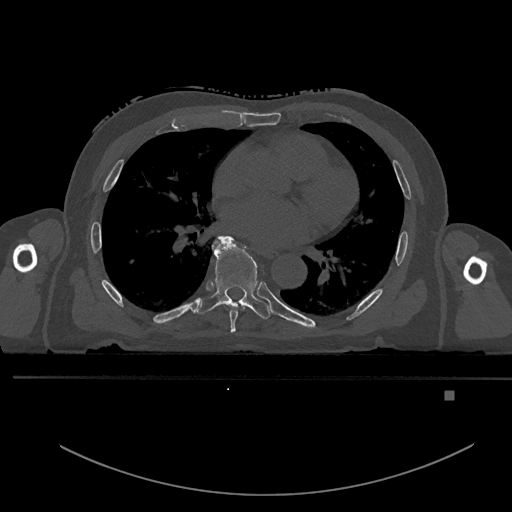
CT including the spine, one axial slice; slice 270 of 969 in the series (ordered by position); bone window (W 1800 / L 400 HU); 0.5 mm slice thickness; 512 × 512 image matrix, field of view 456 × 456 mm. Patient: male, 82 years. From the clinical record (not read from this slice): primary cancer: prostate.
Annotated regions visible in this slice (semi-automatically segmented with operator editing):
- T6 vertebra: bounding box [x1, y1, x2, y2] px = [228, 305, 245, 333]
- T7 vertebra: [197, 235, 271, 320]